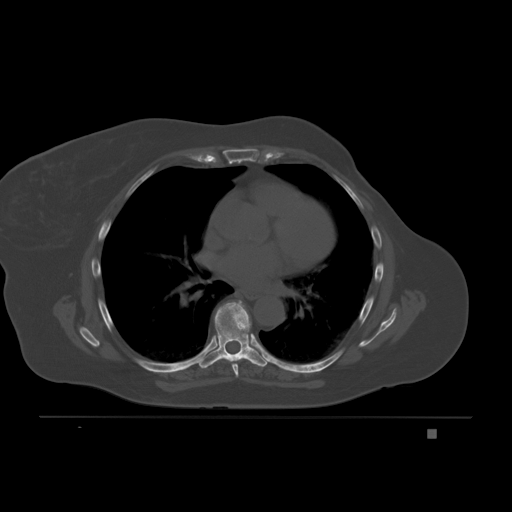
CT including the spine, one axial slice. Slice 130 of 221 in the series (ordered by position). Bone window (W 1800 / L 400 HU). 512 × 512 image matrix. Patient: female, 63 years. Case-level facts recorded for this patient, not image findings: primary cancer: breast.
Annotated regions visible in this slice (semi-automatically segmented with operator editing):
- T6 vertebra: bounding box [x1, y1, x2, y2] px = [232, 363, 239, 378]
- T7 vertebra: [199, 300, 267, 369]